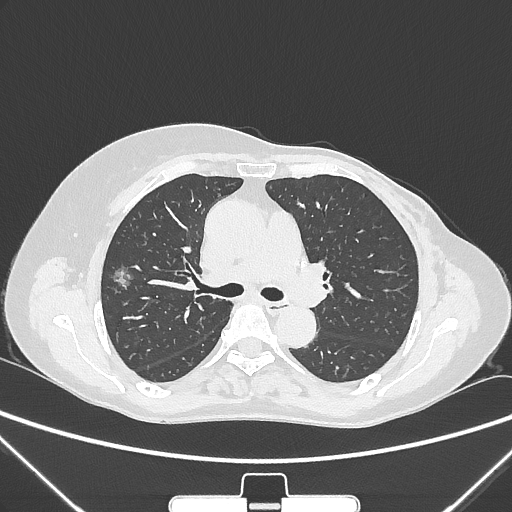
Chest CT, one axial slice; position 160 of 265 along the scan axis; 120 kVp; lung window (W 1500 / L -600 HU); 512 × 512 image matrix, field of view 350 × 350 mm. Patient: female, 64 years. From the clinical record (not read from this slice): clinical TNM (as recorded): T1c N0 M0; histopathological grade: G1-2.
Structures marked on this image (bounding box drawn by a radiologist):
- lung tumour (recorded histology: adenocarcinoma): bounding box <104,255,140,297> (left, top, right, bottom; pixels)